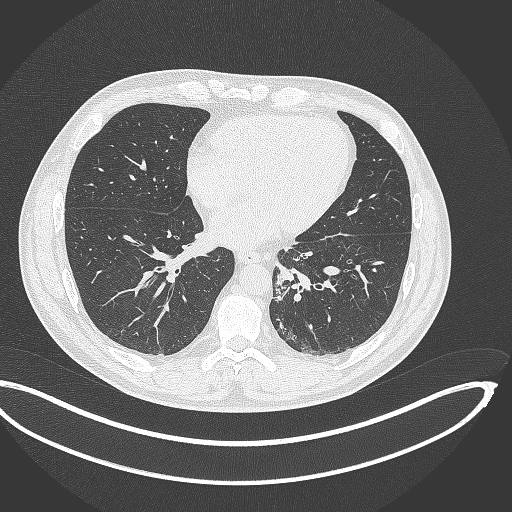
Chest CT, one axial slice; reconstruction kernel B70f; 120 kVp; lung window (W 1500 / L -600 HU); 1 mm slice thickness; 512 × 512 image matrix, field of view 442 × 442 mm. Male patient, age 50 years. Case-level facts recorded for this patient, not image findings: clinical TNM (as recorded): T2a N3 M0.
Annotated regions visible in this slice (bounding box drawn by a radiologist):
- lung tumour (recorded histology: squamous cell carcinoma): box from (x=270, y=272) to (x=294, y=304) px